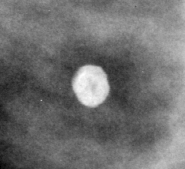
Cropped region of a digitized screen-film mammogram centred on a radiologist-marked abnormality, right breast, MLO view, BI-RADS breast density category 3 (scale 1–4).
Marked abnormality: calcifications, morphology round and regular / eggshell; BI-RADS assessment category 2; subtlety rating 3 on a 1 (subtle) to 5 (obvious) scale; benign; no additional work-up was recommended (benign without callback).